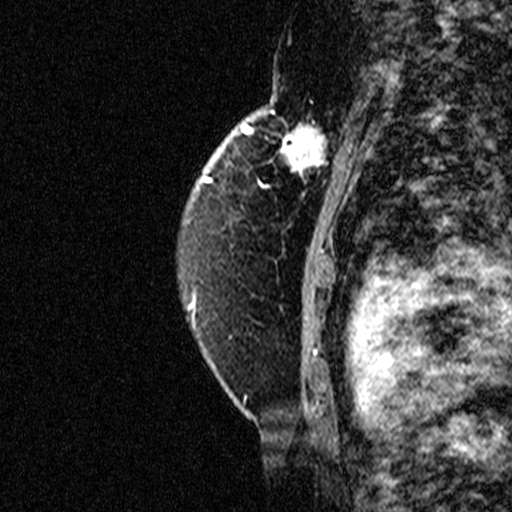
Breast MRI (dynamic contrast-enhanced), one sagittal slice; slice 30 of 44 in the series (ordered by position); dynamic contrast-enhanced study with each time point stored as its own series, time point 2 of 3 at this slice position (early post-contrast, ordered by acquisition time); 1.5 T; TE 4.5 ms, TR 11 ms; 3 mm slice thickness; 512 × 512 image matrix. Female patient, age 49 years. Case-level facts recorded for this patient, not image findings: setting: breast cancer imaged before/during neoadjuvant chemotherapy; receptor status: triple-negative.
Structures marked on this image (semi-automatically segmented with operator editing):
- analysis volume of interest (the breast-tissue region the enhancement analysis was run in; not a lesion): box from (x=254, y=112) to (x=347, y=207) px
- tumour enhancement mask (voxels above the 90 % enhancement threshold inside the analysis volume of interest): (x=254, y=112)–(x=347, y=207)